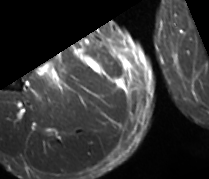
MRI of an extremity soft-tissue mass, one axial slice; slice 21 of 89 in the series (ordered by position); STIR; MR volume resampled by the dataset authors to the PET/CT grid (not the native acquisition matrix); 3.27 mm slice thickness; 209 × 179 image matrix, field of view 204 × 175 mm. Male patient. Case-level facts recorded for this patient, not image findings: histological type: undifferentiated - pleiomorphic; grade: high; site of the primary tumour: right thigh.
Annotated regions visible in this slice (expert contour drawn on MRI and transferred to this co-registered scan by the dataset authors):
- gross tumour volume including surrounding oedema: bounding box <39,62,63,86> (left, top, right, bottom; pixels)